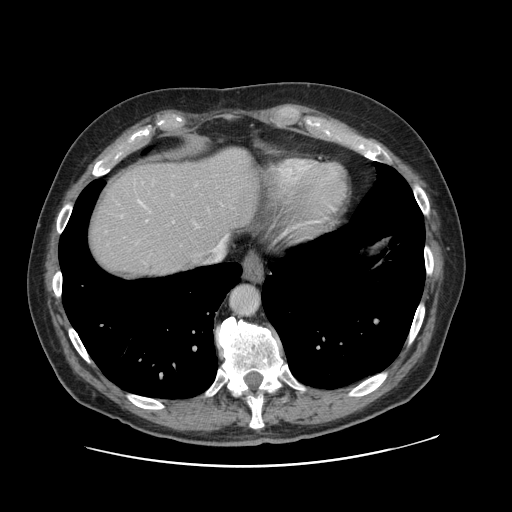
Contrast-enhanced abdominal CT, one axial slice; position 104 of 138 along the scan axis; 120 kVp; soft-tissue window (W 400 / L 40 HU); 2.5 mm slice thickness; 512 × 512 image matrix, field of view 402 × 402 mm. Male patient, age 71 years. From the clinical record (not read from this slice): diagnosis: colorectal cancer liver metastases, imaged before liver resection; multiple liver metastases: no; largest metastasis: 3.3 cm; disease in both lobes: no.
Outlined on this slice (expert manual segmentation):
- hepatic veins: box from (x=140, y=202) to (x=227, y=264) px
- liver: (x=88, y=148)–(x=258, y=280)
- planned liver remnant (the part of the liver to remain after resection): (x=88, y=164)–(x=228, y=280)